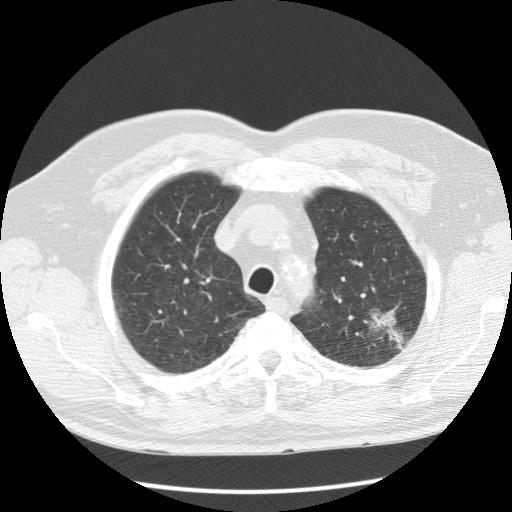
Low-dose screening chest CT, axial slice, baseline screening round, lung window (W 1500 / L -600 HU), 2.5 mm slice thickness, 120 kVp, slice 24 of 123 in the series, 512 × 512 image matrix, field of view 355 × 355 mm. Male, age 60 years at enrolment. Current smoker at enrolment.
• Lesion marked by an expert reader, bounding box <358,299,417,361> (left, top, right, bottom; pixels).
• The screening reader recorded 3 non-calcified nodules or masses ≥4 mm on this exam (left upper lobe, right upper lobe, left upper lobe); which of them this box marks is not recorded.
• Official screen result: positive, change unspecified: nodule(s) >= 4 mm or enlarging nodule(s), mass(es), or other non-specific abnormalities suspicious for lung cancer.
• Later outcome: lung cancer diagnosed 48 days after this screen — bronchiolo-alveolar adenocarcinoma, NOS, left upper lobe, well differentiated (G1), stage IA (AJCC 6th edition), 27 mm at pathology.